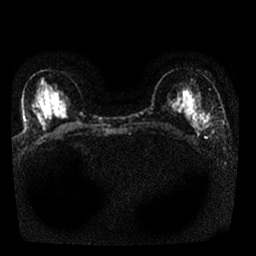
Breast MRI, one axial slice; position 8 of 25 along the scan axis; diffusion-weighted series; image 2 of 4 stored at this slice position (different b-values; order by instance number); 1.5 T; 4 mm slice thickness; 256 × 256 image matrix. Female patient.
Outlined on this slice (manually delineated by an expert):
- tumour on diffusion-weighted imaging: bounding box (x1, y1, x2, y2) in pixels: (203, 119, 208, 127)